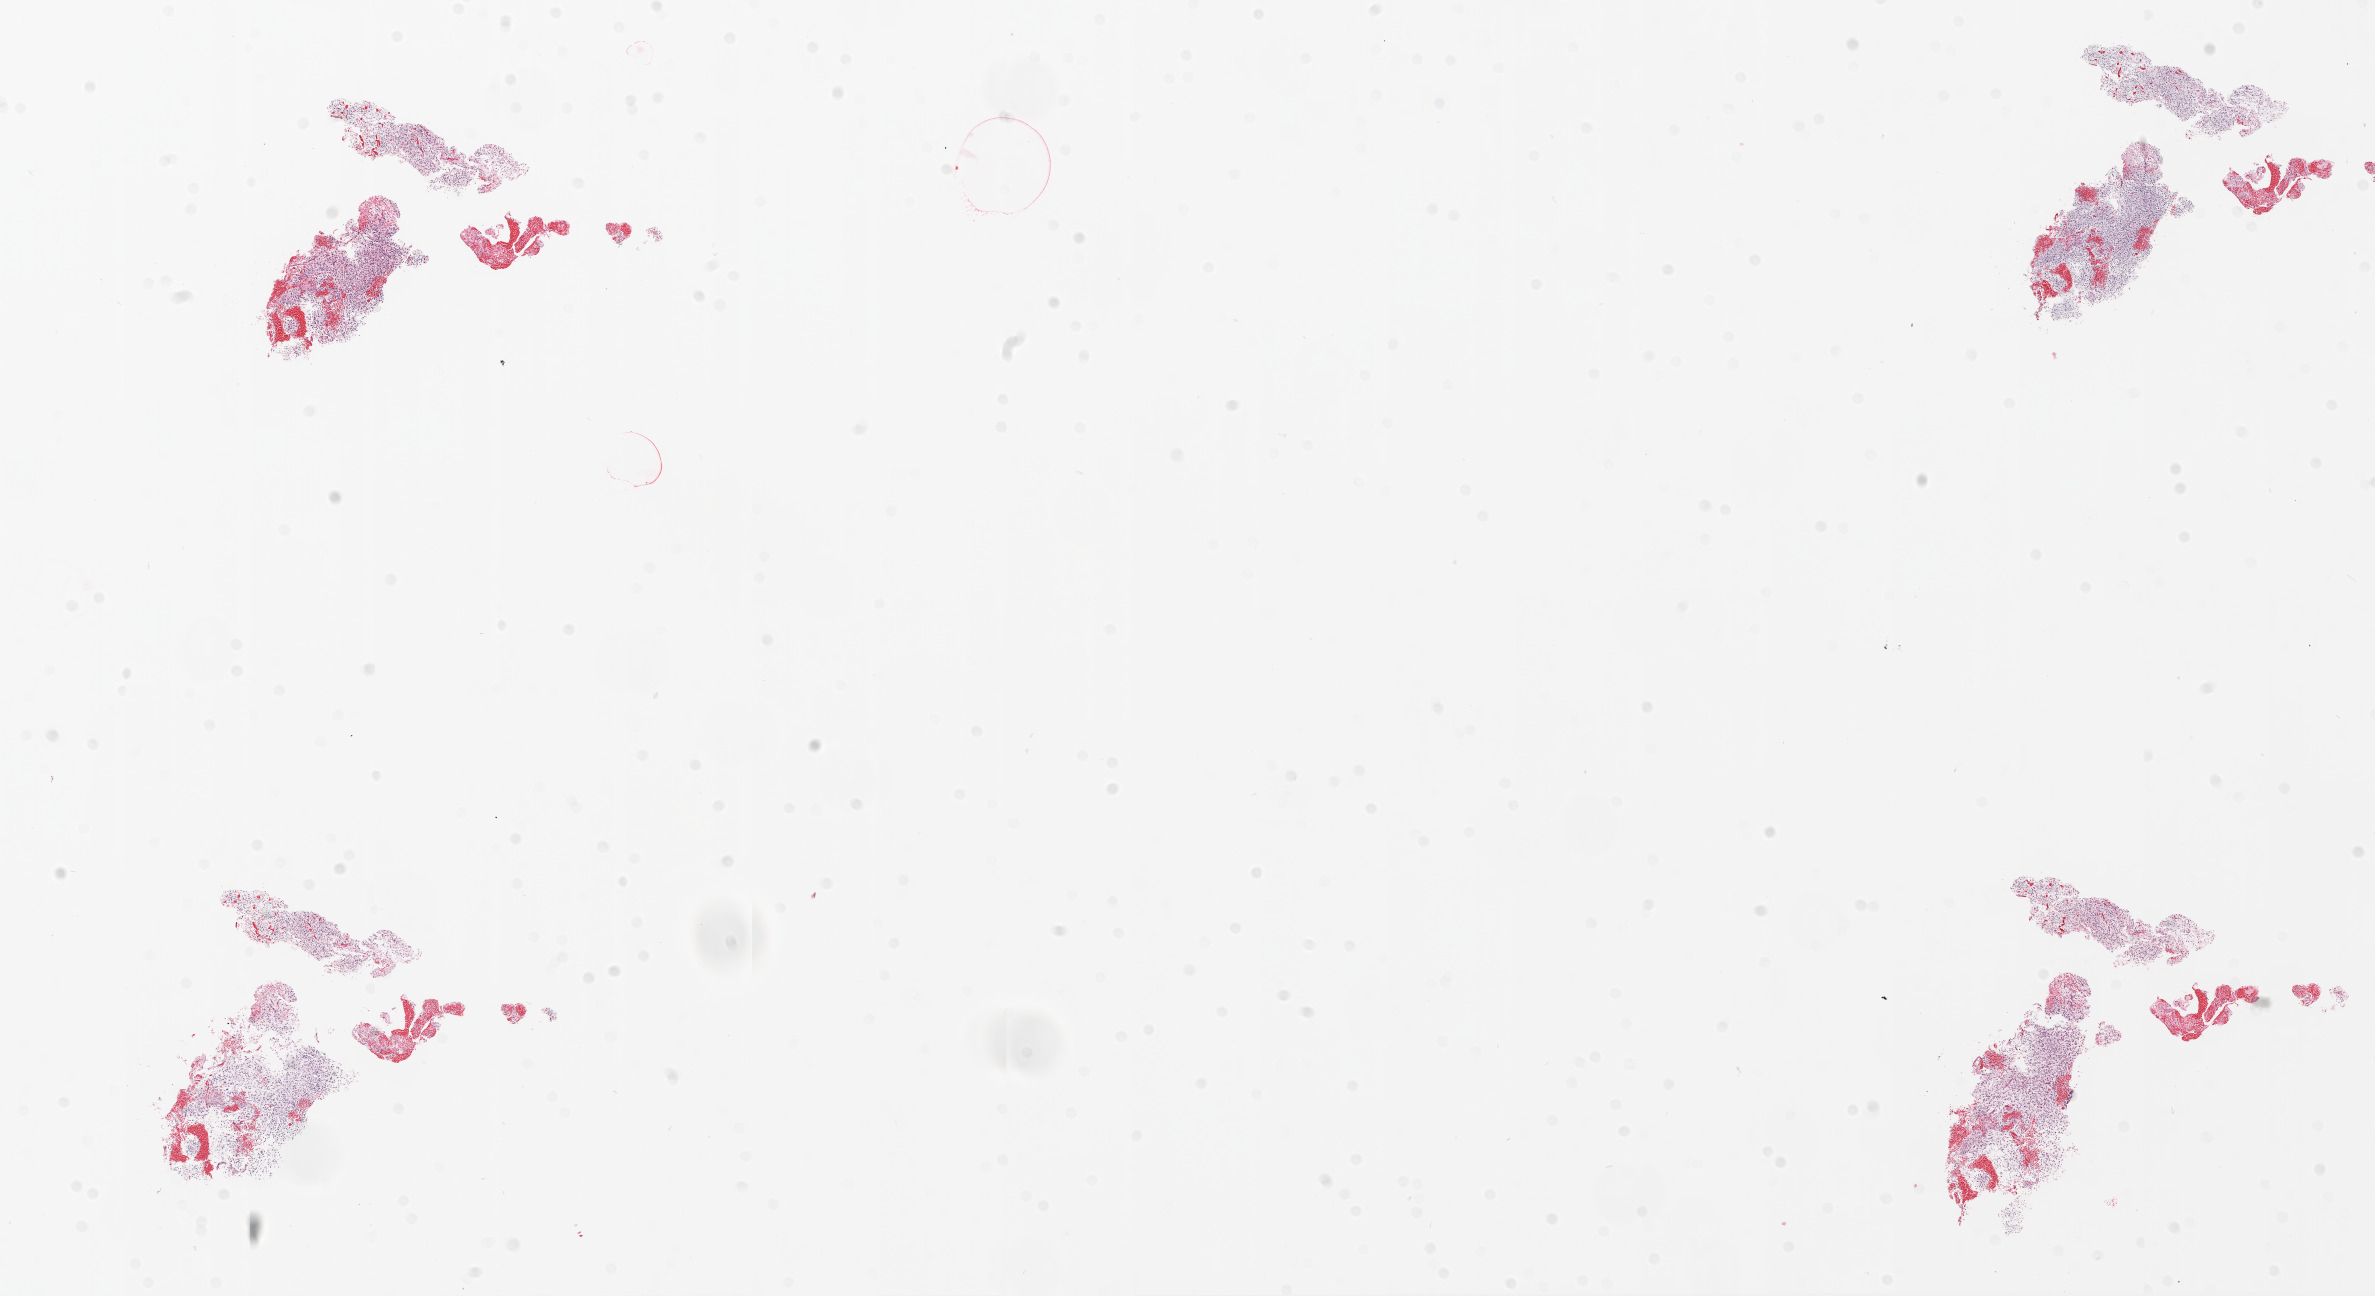
Whole-slide histology image, Hematoxylin and eosin (H&E) stained, whole scanned area (about 19.1 x 10.4 mm, slide scanned at 20x) shown as a low-resolution overview. Formalin-fixed paraffin-embedded (FFPE) diagnostic section. Primary tumour sample from the brain. Male patient; age at initial diagnosis 61 years.
Pathologic diagnosis: Glioblastoma.